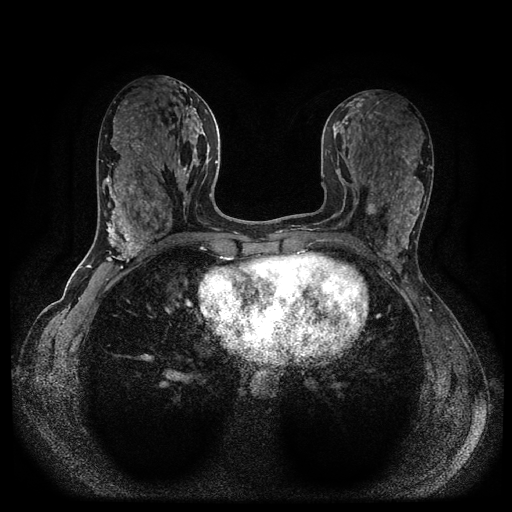
Breast MRI (dynamic contrast-enhanced, multi-phase), one axial slice; dynamic contrast-enhanced series, time point 2 of 5 at this slice position (early post-contrast); 1.5 T; TE 2.6 ms, TR 5.4 ms; 2 mm slice thickness; 512 × 512 image matrix, field of view 340 × 340 mm. Patient: female, 43 years.
Structures marked on this image (semi-automatic segmentation, software-assisted and operator-edited):
- breast lesion (labelled benign in the annotation): bounding box <365,199,379,216> (left, top, right, bottom; pixels)